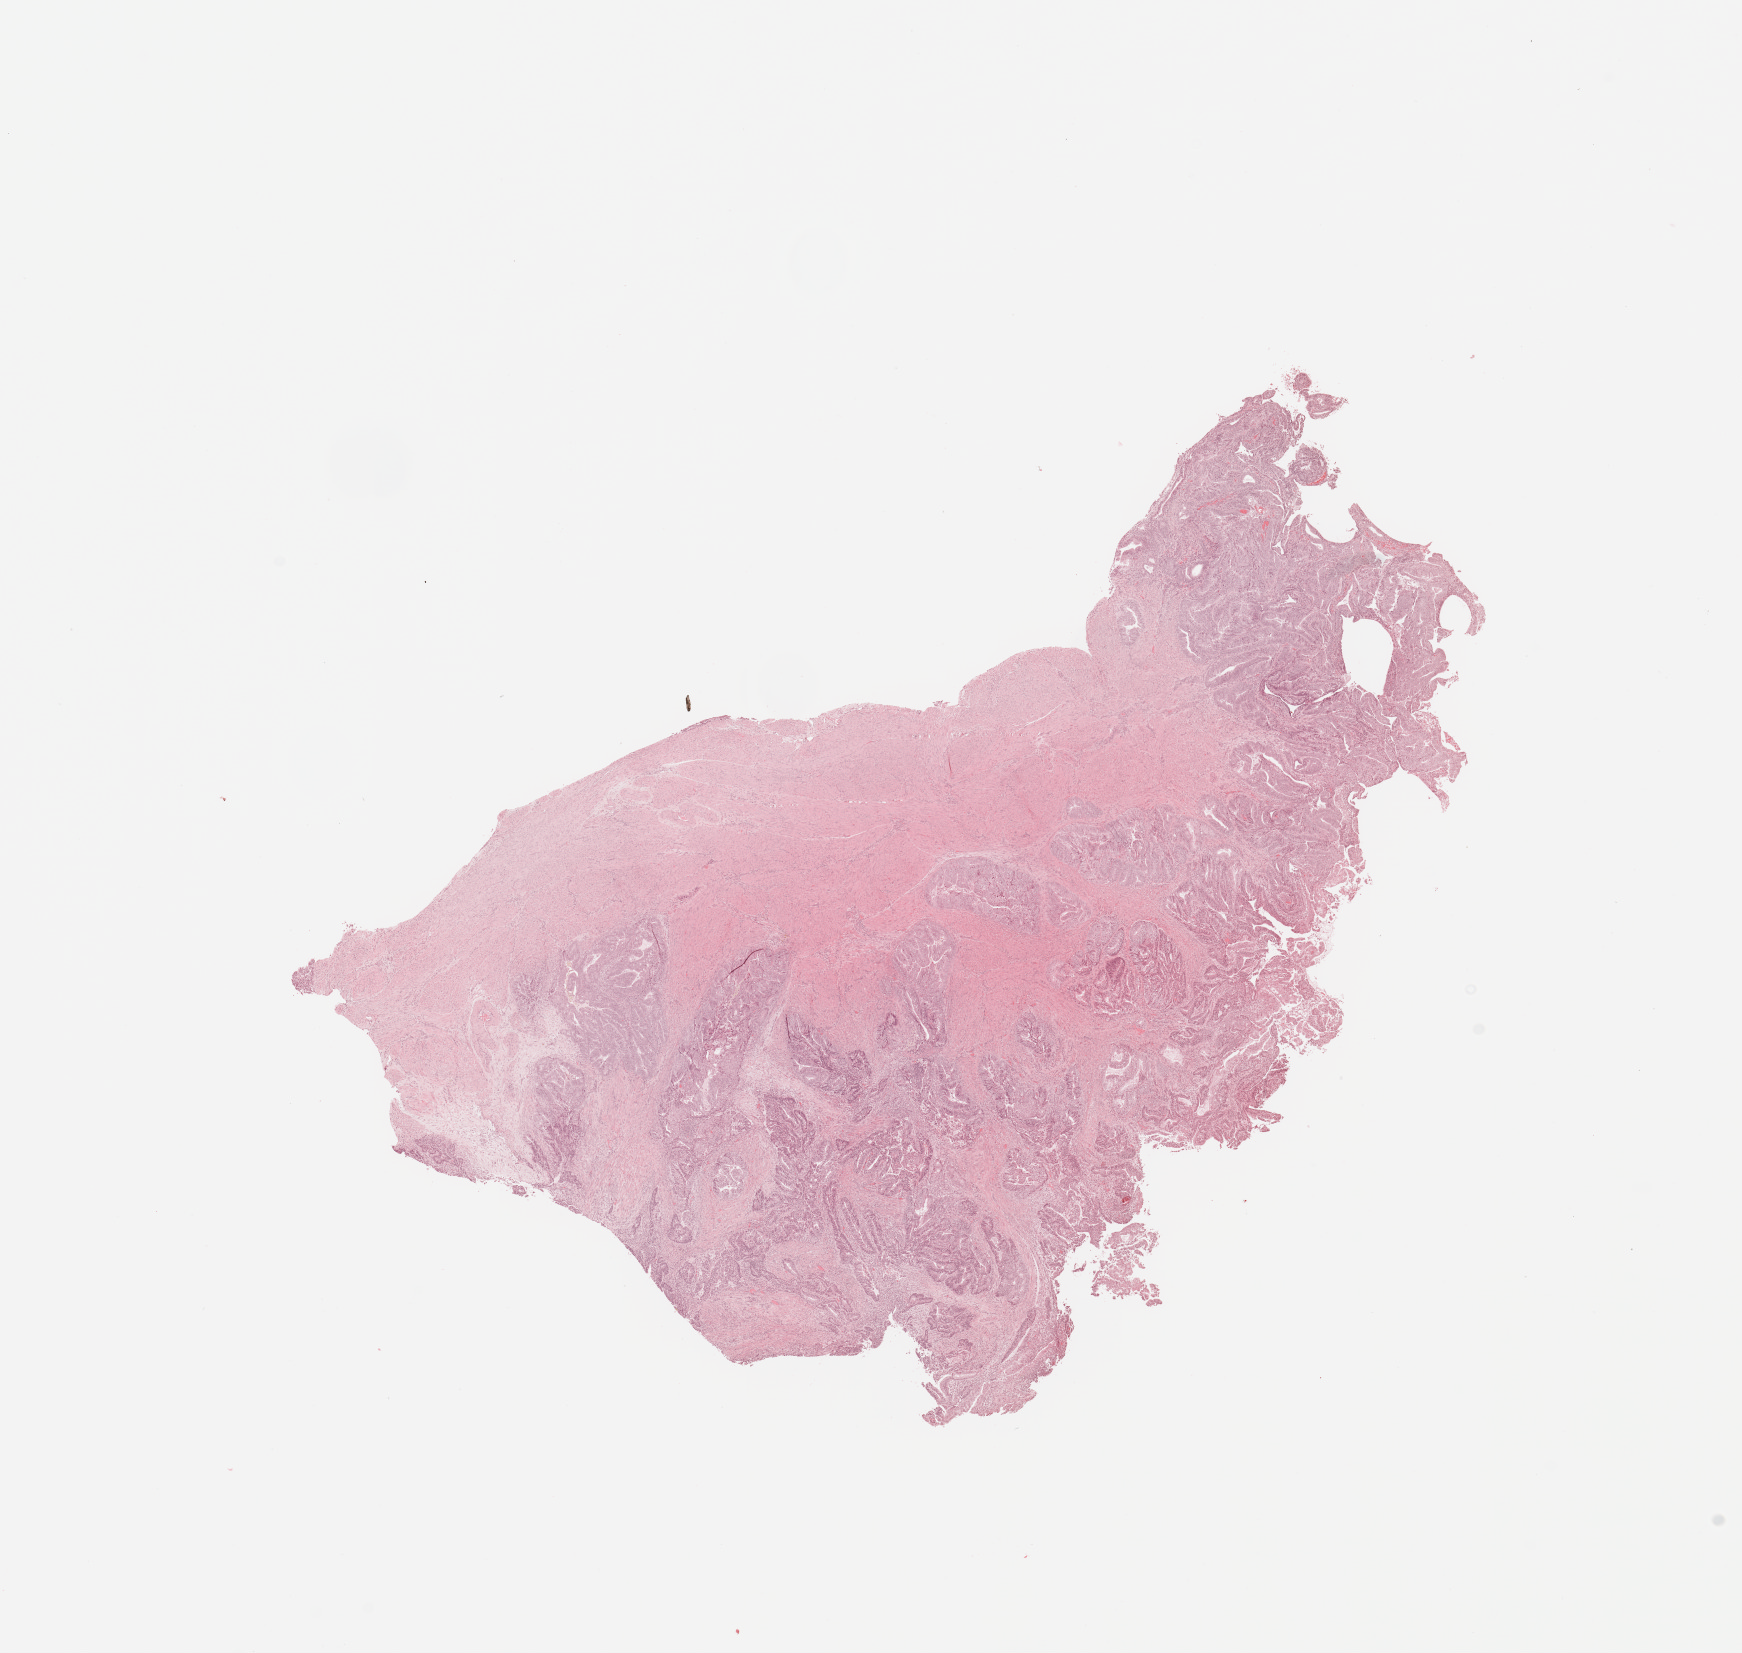
Hematoxylin and eosin (H&E) stained whole-slide image, shown as a low-resolution overview of the whole scanned area (about 13.8 x 13.1 mm). Tumour tissue sample, sampled site: uterus. Patient: female, age 56 years. Histologic grade: G2 (moderately differentiated). Pathologist review of this section (percent, as recorded): tumour nuclei 80%, necrosis 1%.
AJCC pathologic stage: I. Histologic diagnosis: Endometrioid adenocarcinoma, NOS. Primary tumour site (as recorded): anterior endometrium.